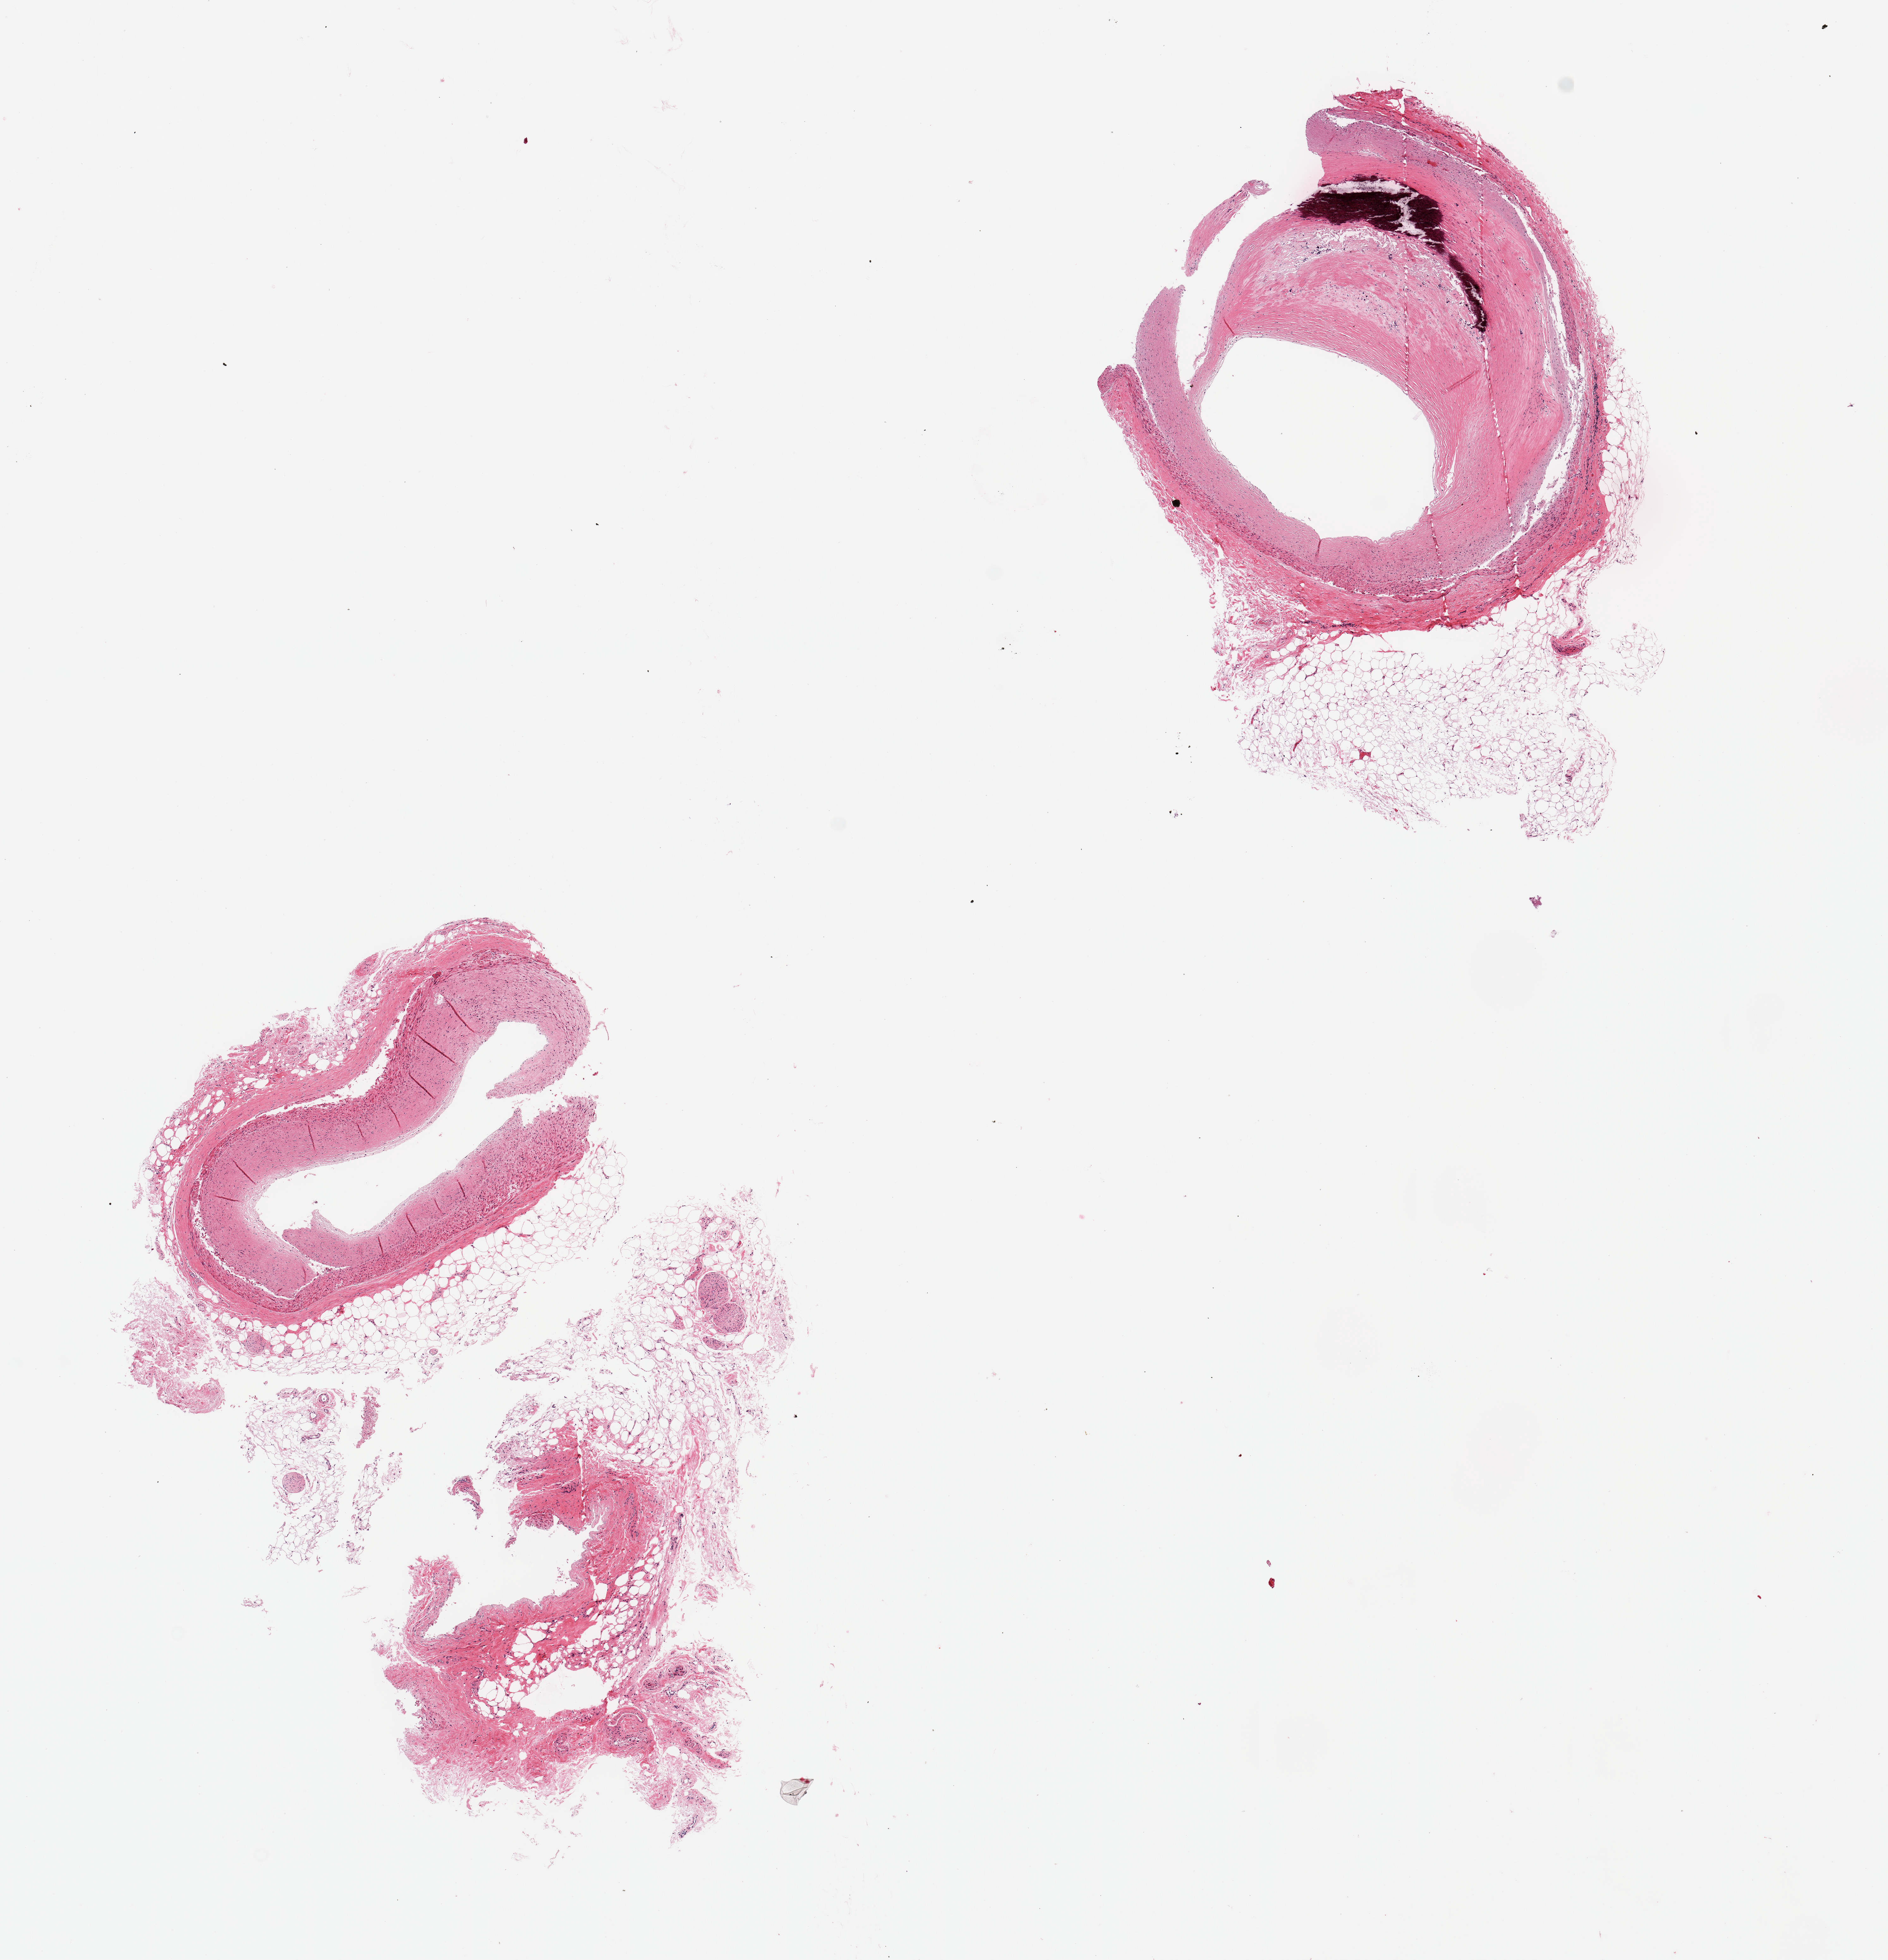
Digitized haematoxylin and eosin-stained section, brightfield, shown as a low-resolution overview of the whole scanned area (about 11.8 x 12.3 mm, acquisition: 20x scan), PAXgene-fixed paraffin-embedded (PFPE) section, target tissue: coronary artery, tissue donor sample.
- pathologist's review note for this sample: 2 pieces; one piece fragmented (has attached fat/vessel/nerve) and other shows calcification and atherosclerotic plaque compromising the lumen (50-75%), 1.4mm of attached fat